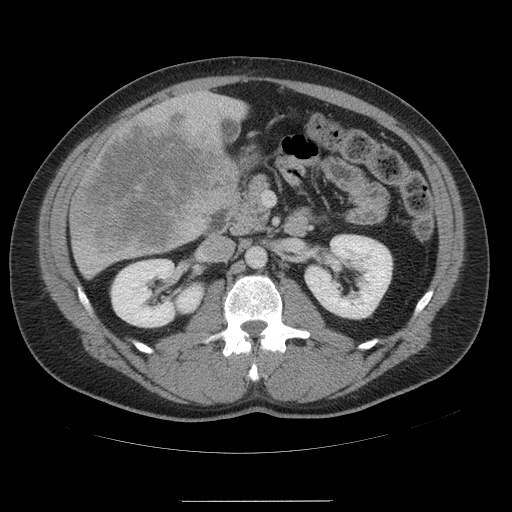
Contrast-enhanced abdominal CT, one axial slice. Position 22 of 54 along the scan axis. 120 kVp. Intravenous contrast given. Soft-tissue window (W 400 / L 40 HU). 5 mm slice thickness. 512 × 512 image matrix. Male patient, age 40 years. From the clinical record (not read from this slice): diagnosis: colorectal cancer liver metastases, imaged before liver resection; multiple liver metastases: no; largest metastasis: 15 cm; disease in both lobes: no.
Outlined on this slice (manually delineated by an expert):
- liver: bounding box (x1, y1, x2, y2) in pixels: (70, 92, 245, 279)
- planned liver remnant (the part of the liver to remain after resection): (234, 101, 246, 115)
- liver metastasis: (69, 110, 237, 258)